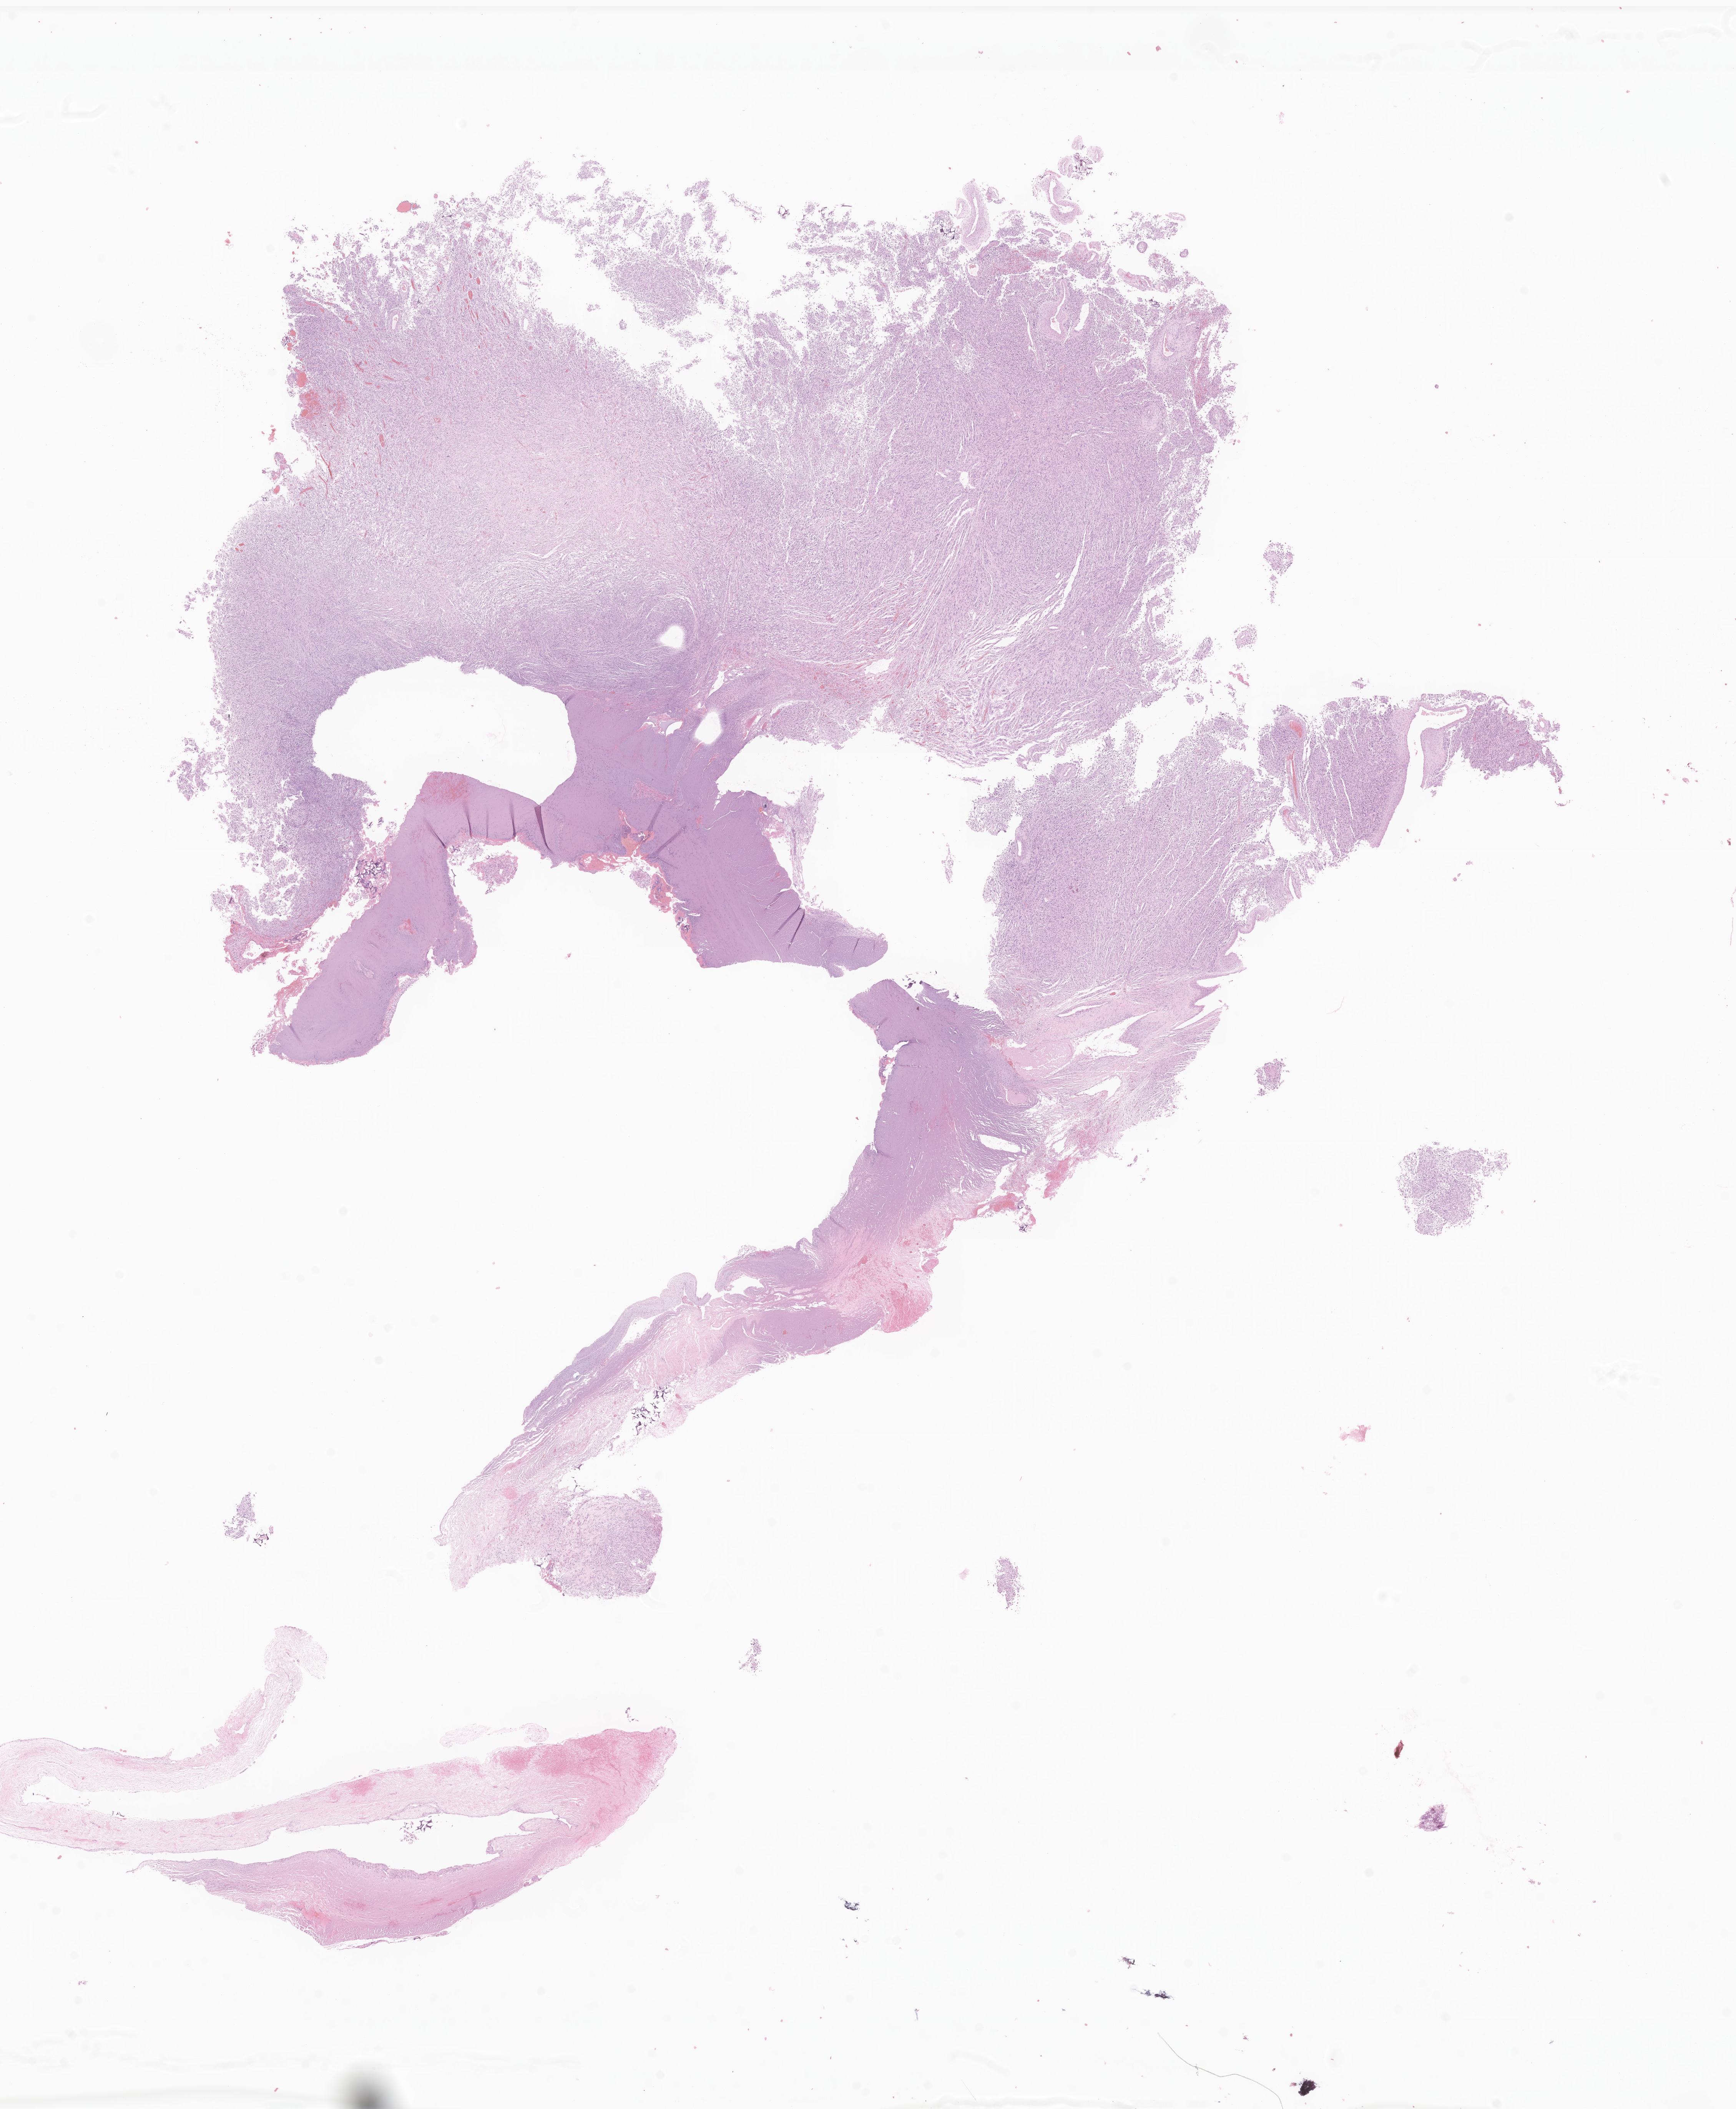
Digitized H&E-stained section of tumor tissue from the brain, shown as a low-resolution overview of the whole scanned area (about 19.0 x 23.1 mm), formalin-fixed paraffin-embedded section. Patient female; age 82 months (6 years 10 months).
Recorded diagnosis: Glioma, malignant.